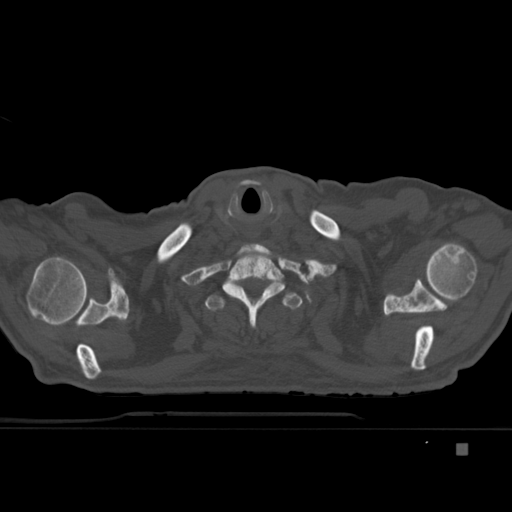
CT including the spine, one axial slice. Position 357 of 451 along the scan axis. Bone window (W 1800 / L 400 HU). 1.5 mm slice thickness. 512 × 512 image matrix. Male patient, age 75 years. Case-level facts recorded for this patient, not image findings: primary cancer: prostate.
Structures marked on this image (semi-automatically segmented with operator editing):
- T1 vertebra: bounding box [x1, y1, x2, y2] px = [222, 243, 285, 328]
- T2 vertebra: [205, 292, 303, 311]